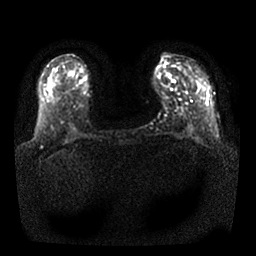
Breast MRI, one axial slice; position 13 of 25 along the scan axis; diffusion-weighted series; image 2 of 4 stored at this slice position (different b-values; order by instance number); 1.5 T; 4 mm slice thickness; 256 × 256 image matrix, field of view 340 × 340 mm. Female patient.
Annotated regions visible in this slice (expert manual segmentation):
- tumour on diffusion-weighted imaging: bounding box [x1, y1, x2, y2] px = [79, 74, 87, 81]